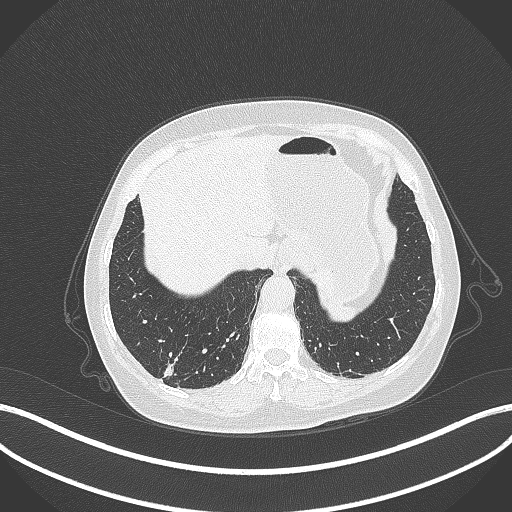
Chest CT, one axial slice; slice 45 of 333 in the series (ordered by position); lung window (W 1500 / L -600 HU); 1 mm slice thickness; 512 × 512 image matrix. Patient: female, 69 years. From the clinical record (not read from this slice): clinical TNM (as recorded): T1b N0 M0; histopathological grade: G2-3.
Outlined on this slice (bounding box drawn by a radiologist):
- lung tumour (recorded histology: adenocarcinoma): bounding box (x1, y1, x2, y2) in pixels: (158, 358, 176, 379)